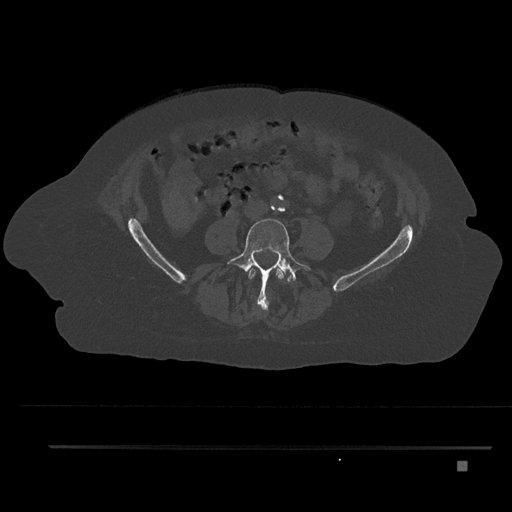
CT including the spine, one axial slice. Position 85 of 797 along the scan axis. Reconstruction kernel Br40s/3. Bone window (W 1800 / L 400 HU). 0.5 mm slice thickness. 512 × 512 image matrix, field of view 437 × 437 mm. Female patient, age 76 years. Case-level facts recorded for this patient, not image findings: primary cancer: lung; vertebrae with lytic lesions (as recorded): T11, L3.
Annotated regions visible in this slice (semi-automatic segmentation, software-assisted and operator-edited):
- L3 vertebra: bounding box [x1, y1, x2, y2] px = [248, 268, 284, 309]
- L4 vertebra: [226, 218, 311, 311]
- L5 vertebra: [288, 272, 293, 281]